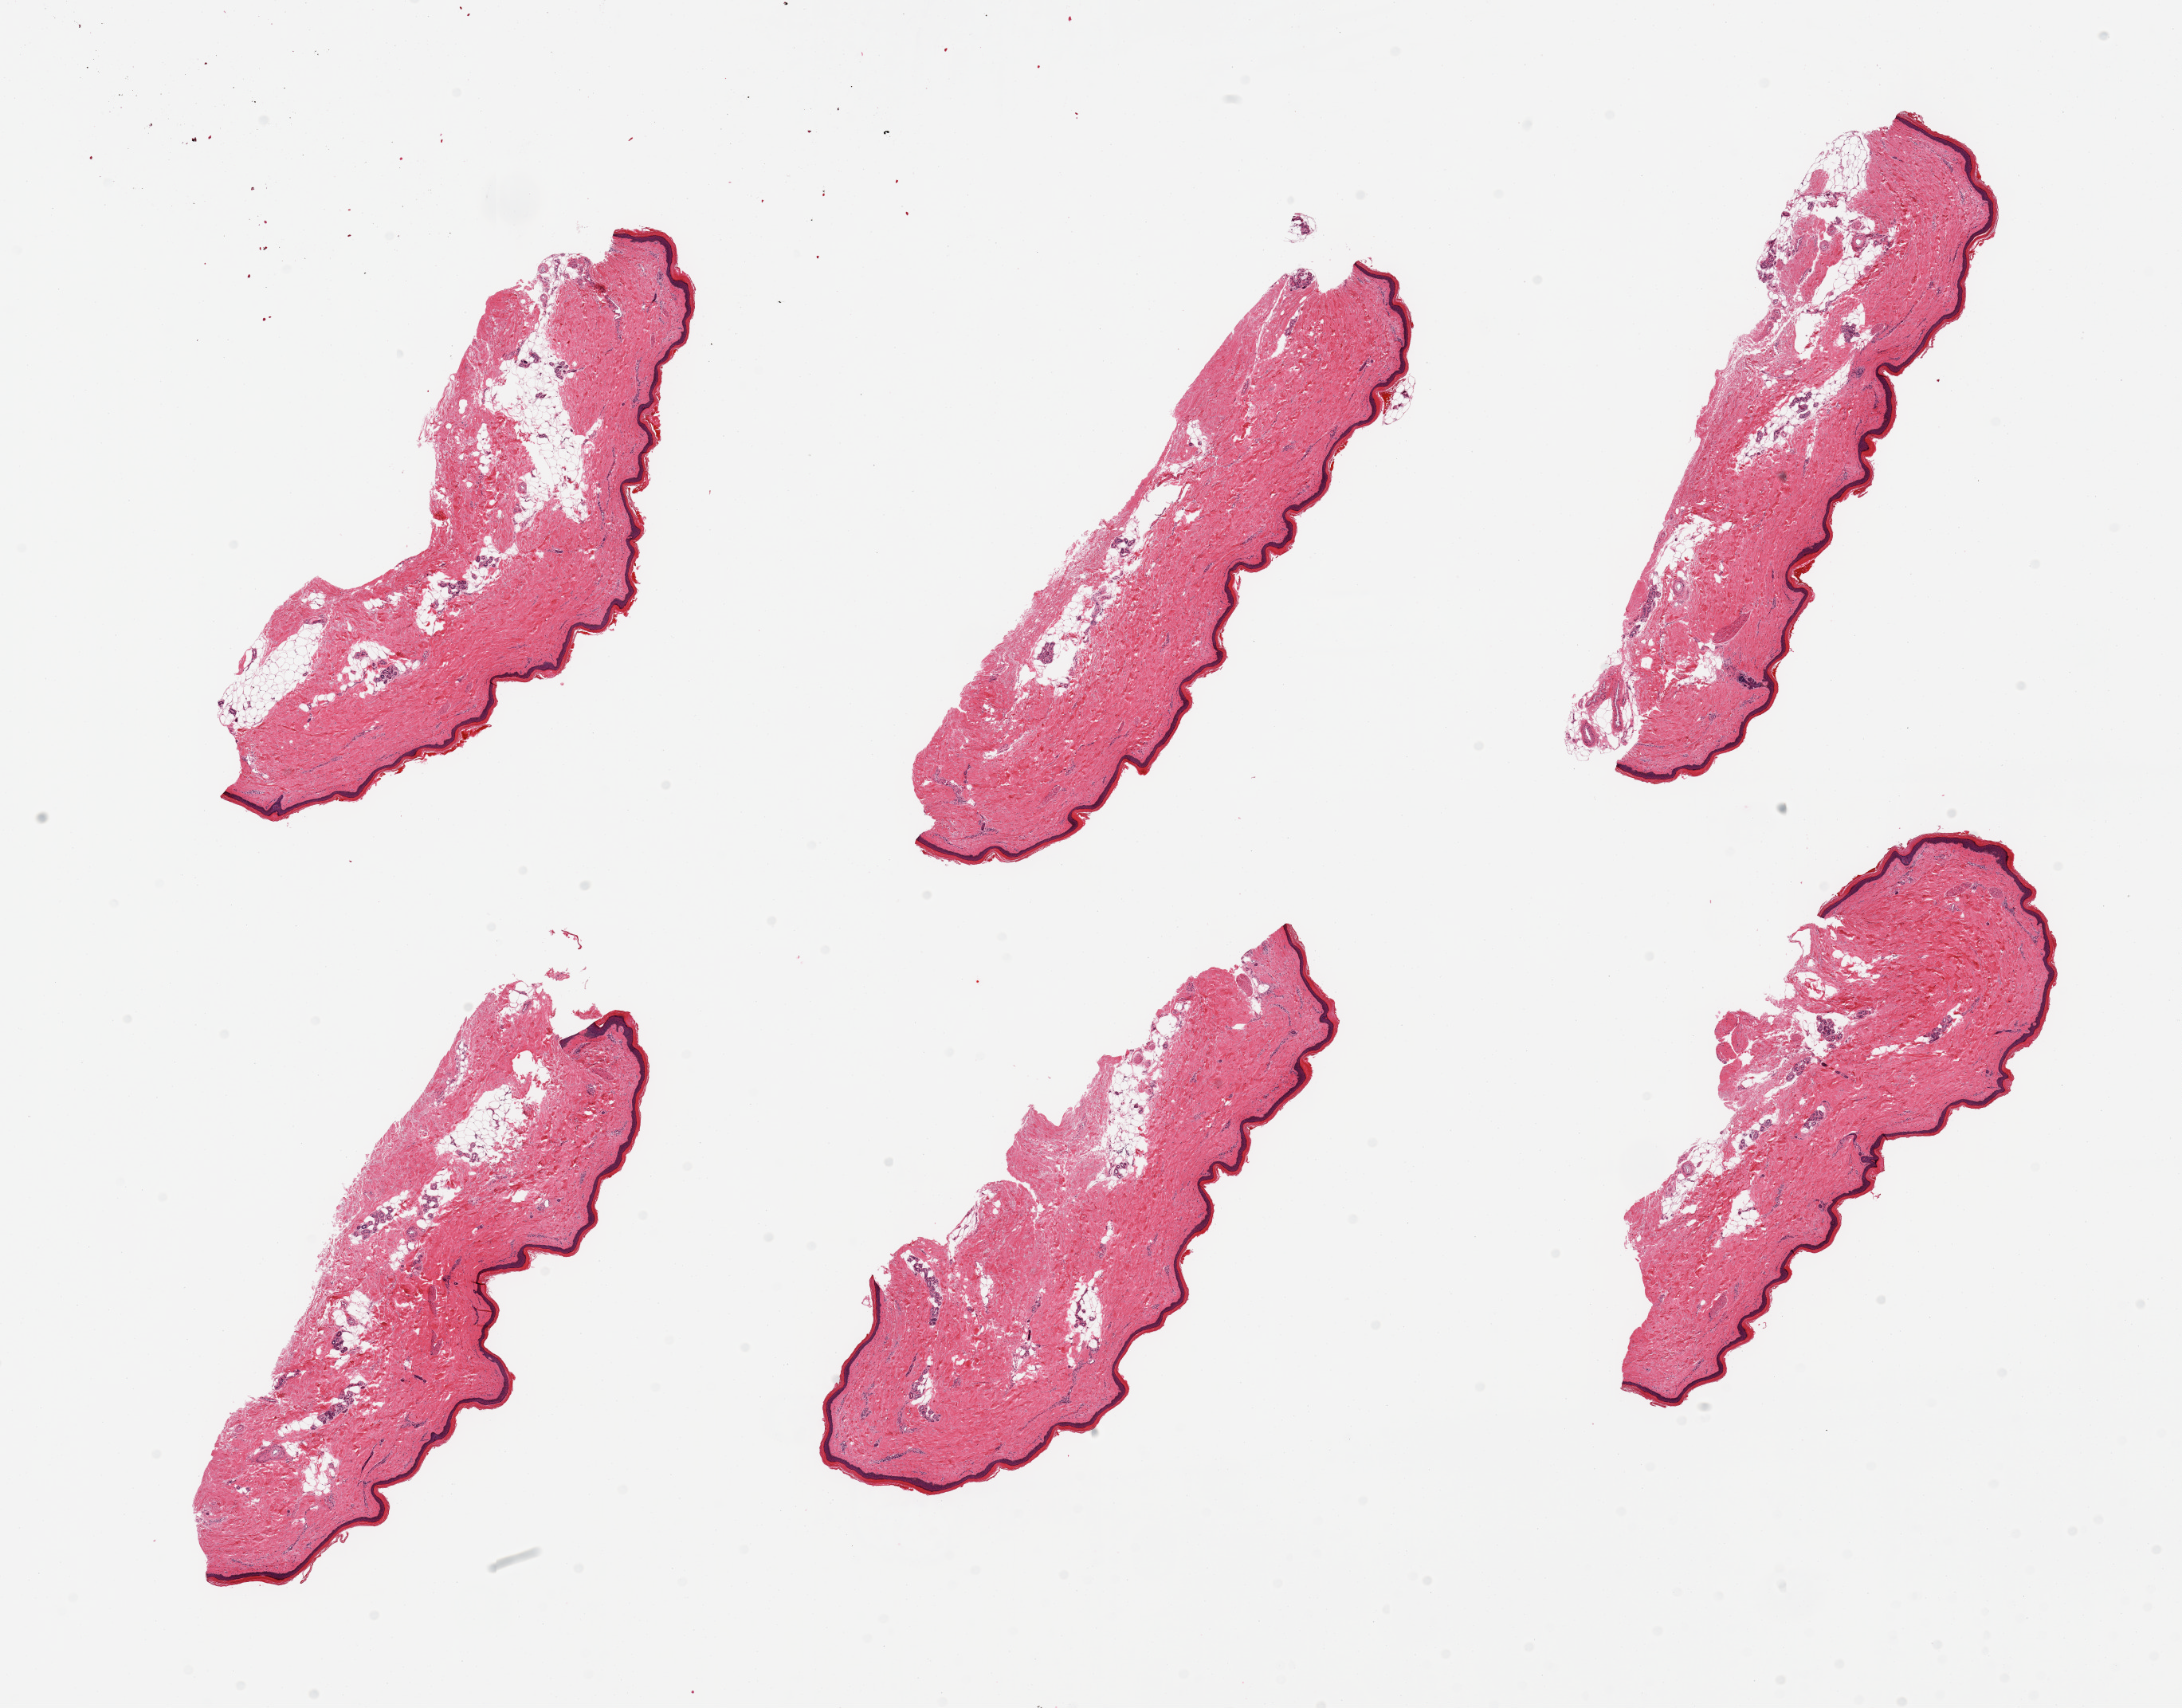
H&E whole-slide image, a low-resolution overview of the entire scanned area, about 21.7 x 17.0 mm, PAXgene-fixed paraffin-embedded (PFPE) section, target tissue: skin of lower leg, tissue donor sample. Female donor.
Pathologist's review note for this sample: 6 pieces, trace dermal fat. Squamous epithelium is ~50 microns.